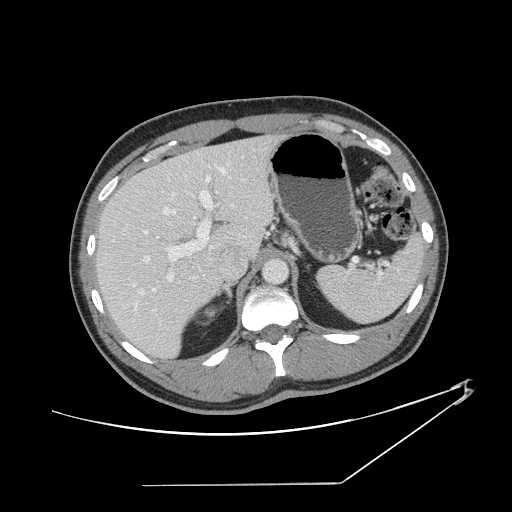
Contrast-enhanced abdominal CT, one axial slice. Slice 95 of 152 in the series (ordered by position). 120 kVp. Soft-tissue window (W 400 / L 40 HU). 2.5 mm slice thickness. 512 × 512 image matrix, field of view 432 × 432 mm. Male patient, age 45 years. Case-level facts recorded for this patient, not image findings: diagnosis: colorectal cancer liver metastases, imaged before liver resection; multiple liver metastases: no; largest metastasis: 1 cm.
Structures marked on this image (manually delineated by an expert):
- hepatic veins: bounding box (x1, y1, x2, y2) in pixels: (111, 160, 234, 295)
- liver: (98, 137, 274, 357)
- planned liver remnant (the part of the liver to remain after resection): (98, 154, 228, 357)
- portal vein (with intrahepatic branches): (143, 176, 213, 325)